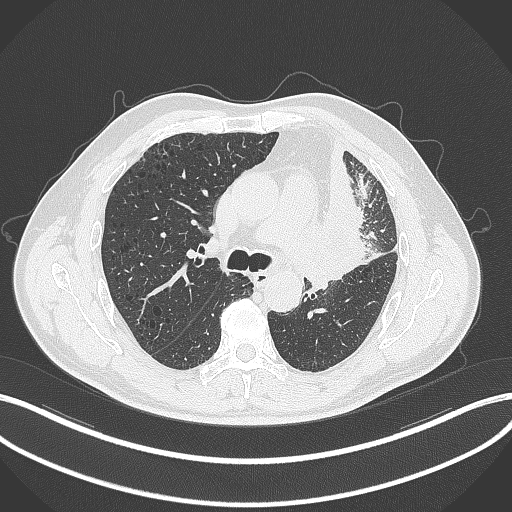
Chest CT, one axial slice; position 192 of 297 along the scan axis; reconstruction kernel B70f; lung window (W 1500 / L -600 HU); 1 mm slice thickness; 512 × 512 image matrix. Male patient, age 68 years. From the clinical record (not read from this slice): clinical TNM (as recorded): T3 N3 M1.
Structures marked on this image (bounding box drawn by a radiologist):
- lung tumour (recorded histology: adenocarcinoma): bounding box (x1, y1, x2, y2) in pixels: (317, 181, 380, 299)